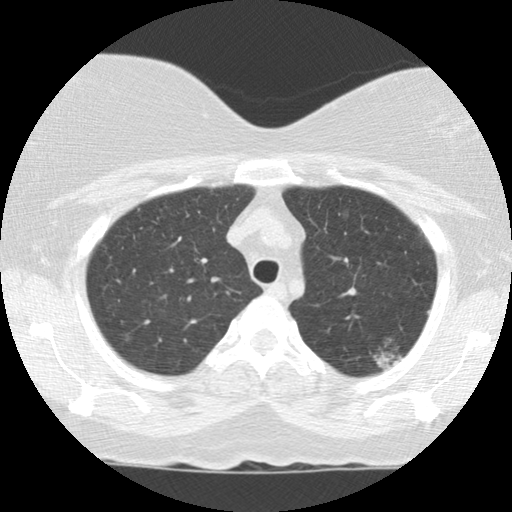
Chest CT (low-dose screening protocol), one axial image, baseline screening round, lung window (W 1500 / L -600 HU), 2.5 mm slice thickness, 512 × 512 image matrix. Female participant, aged 56 years at enrolment. Current smoker at enrolment.
Lesion marked by an expert reader, bounding box (x1, y1, x2, y2) in pixels: (356, 319, 419, 384). The screening reader recorded 4 non-calcified nodules or masses ≥4 mm on this exam (left upper lobe, left upper lobe, right upper lobe, left upper lobe); which of them this box marks is not recorded.